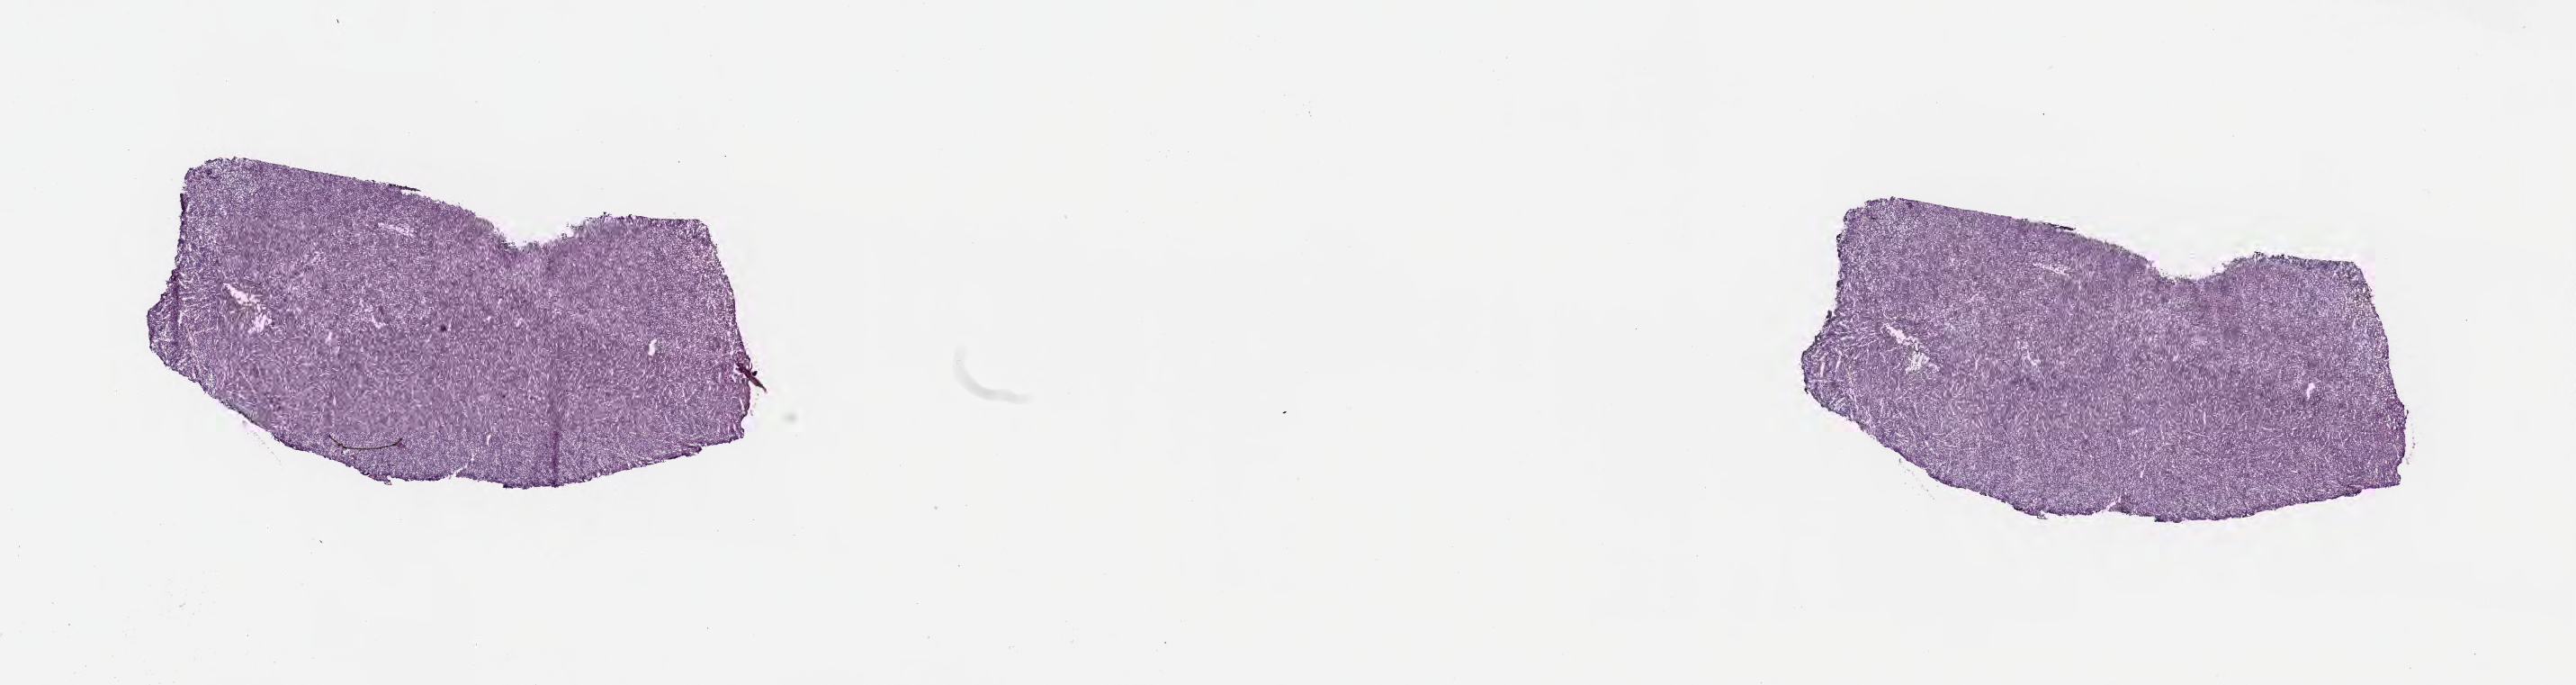
Haematoxylin and eosin whole-slide image, a low-resolution overview of the entire scanned area, about 23.1 x 6.1 mm. Frozen section. Specimen: primary tumor. Anatomic site: cranium. Male, age 4 years at initial diagnosis. Pathologist review of this section (percent, as recorded): tumor cells 95%, tumor nuclei 95%, stromal cells 5%, necrosis 0%, normal cells 0%. Inflammatory infiltration, as recorded: lymphocyte infiltration 40%, monocyte infiltration 35%, neutrophil infiltration 5%.
Ann Arbor stage (patient): Stage IV. Histologic diagnosis: Burkitt lymphoma, NOS.